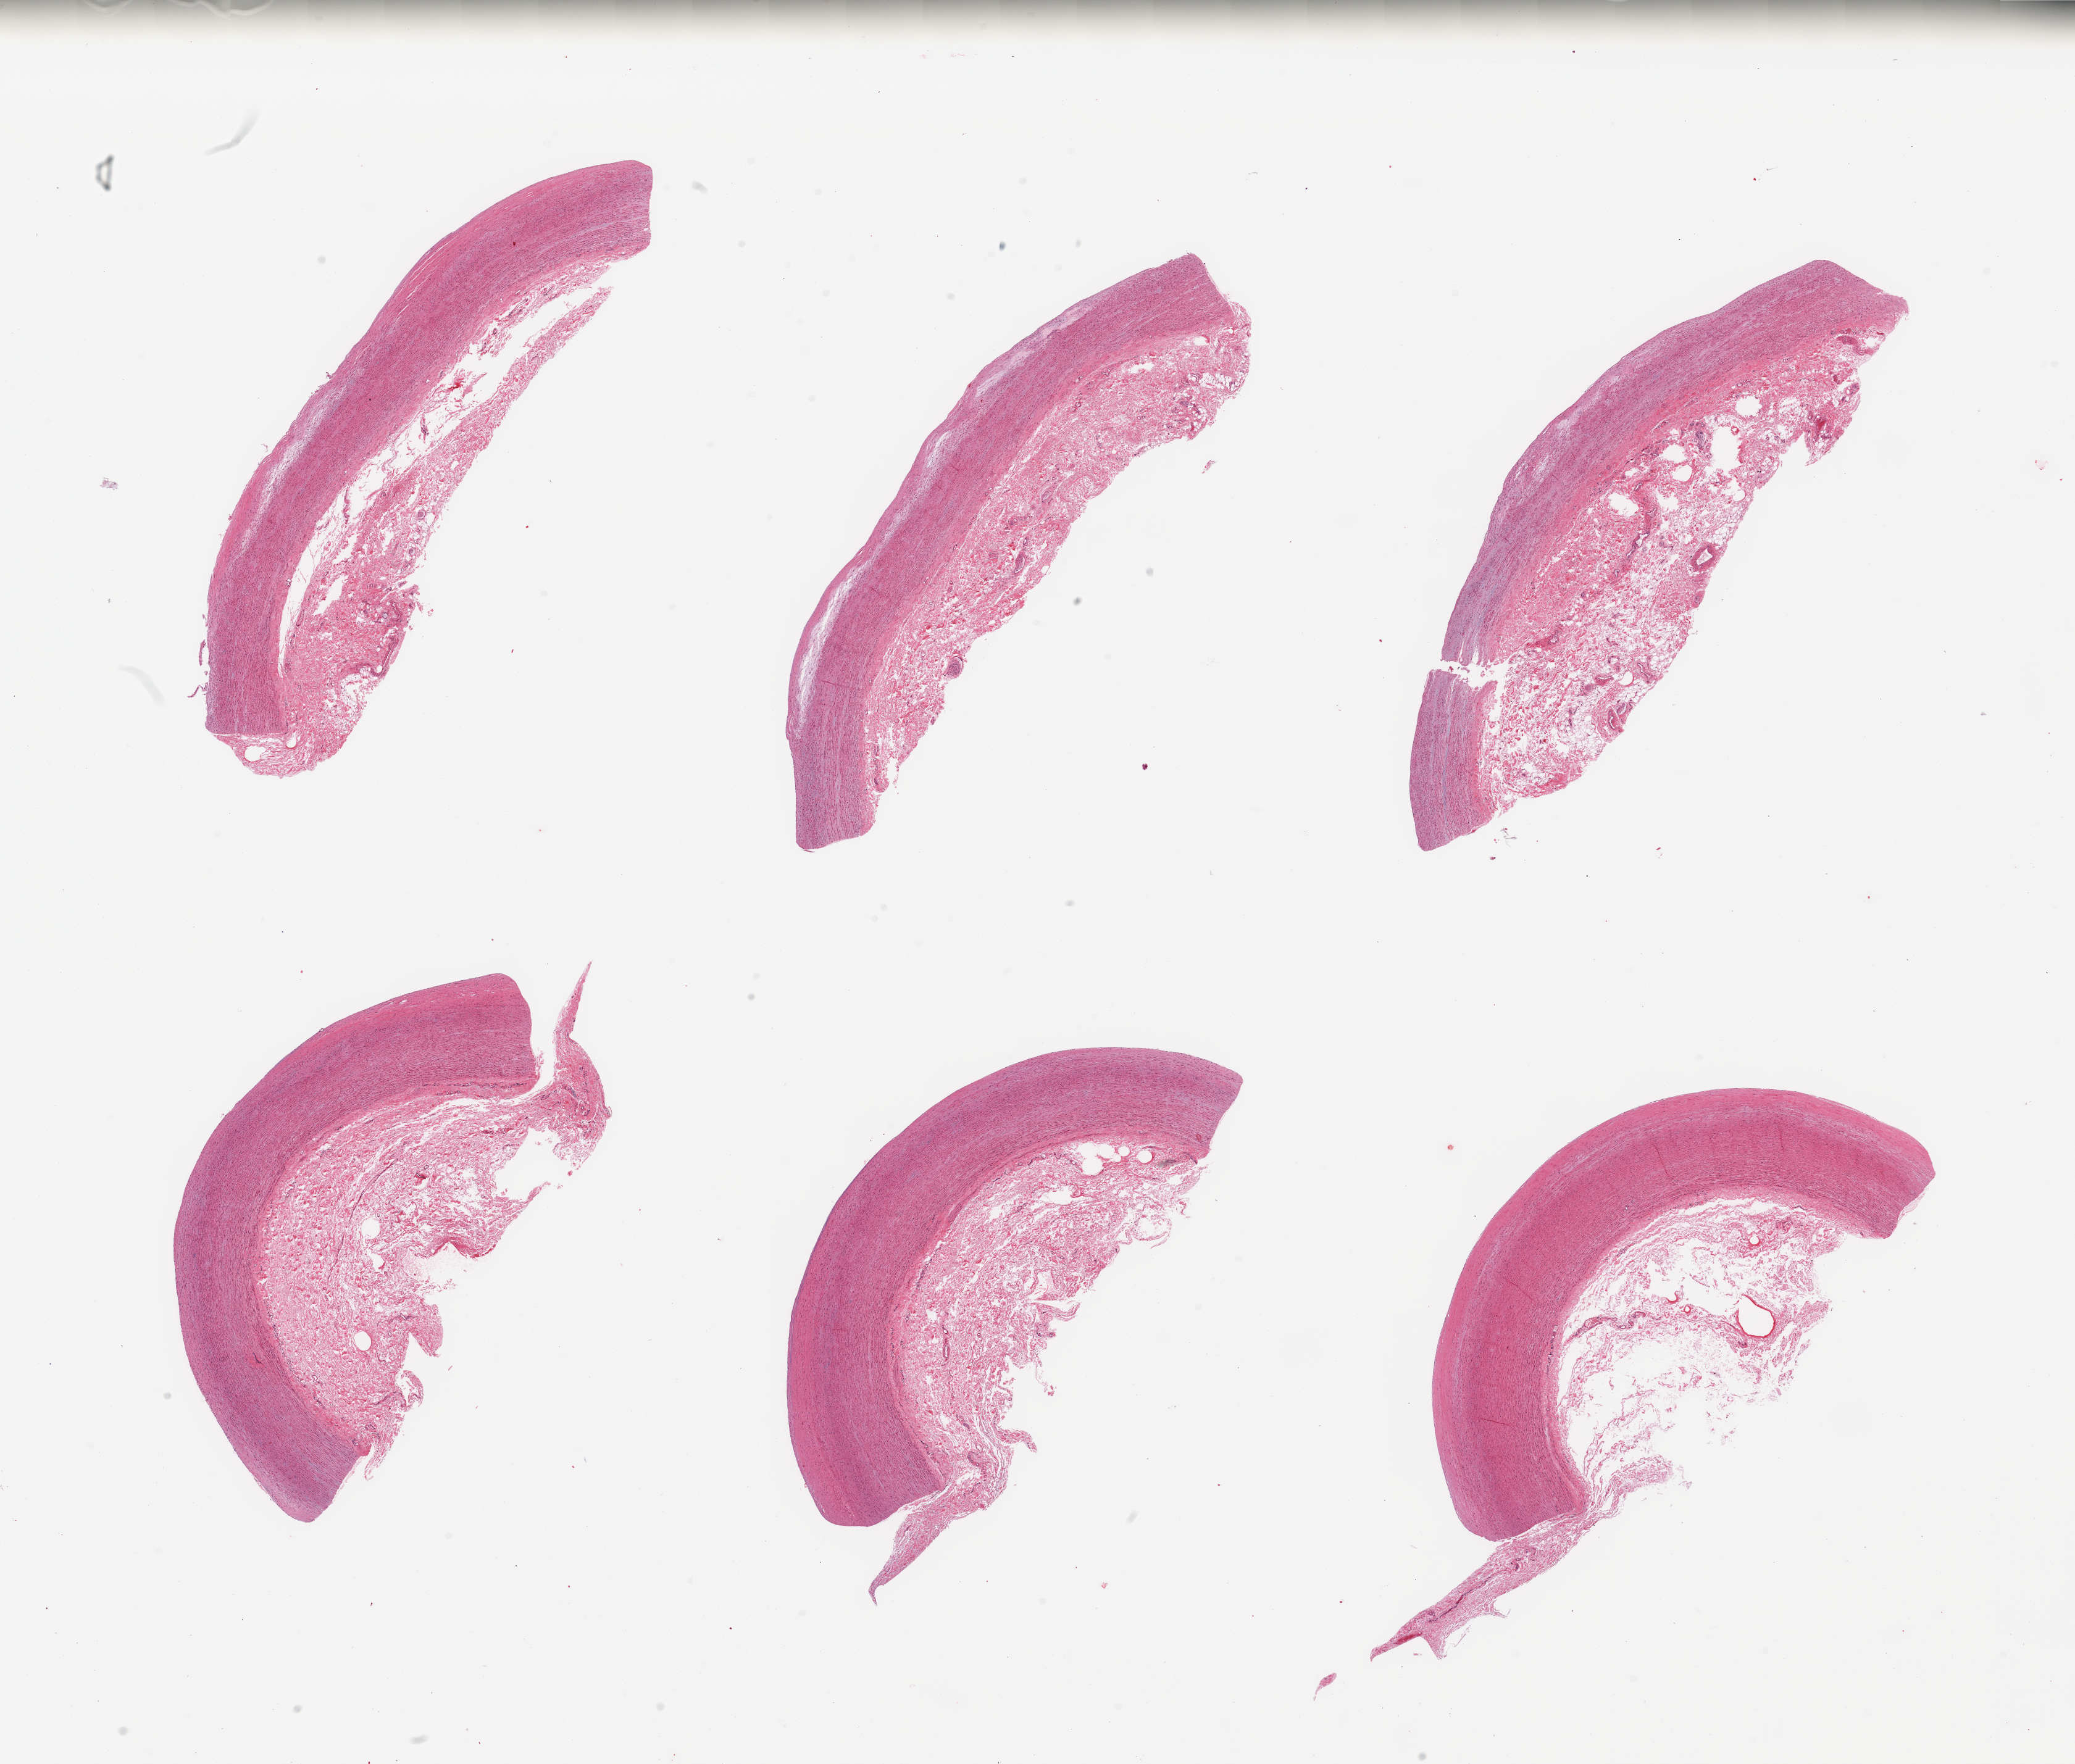
Digitized hematoxylin and eosin (H&E)-stained section — a low-resolution overview of the entire scanned area, about 26.6 x 22.6 mm; PAXgene-fixed, paraffin-embedded tissue; section of aorta (target tissue); tissue donor sample. Donor sex: male.
• pathologist's review note for this sample: 6 pieces; atherosis up to ~0.4mm; adherent fat to ~4mm